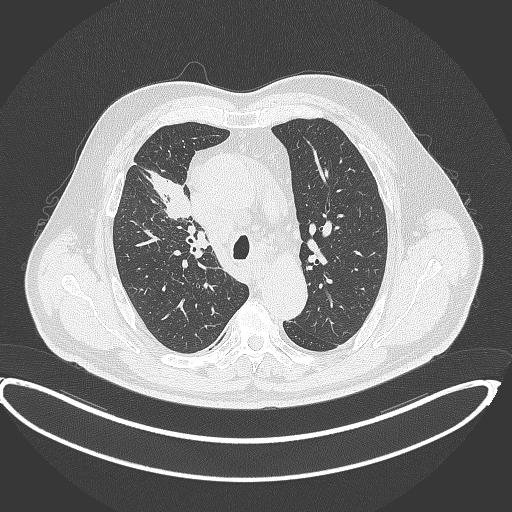
Chest CT, one axial slice. Position 285 of 390 along the scan axis. Lung window (W 1500 / L -600 HU). 1 mm slice thickness. 512 × 512 image matrix, field of view 448 × 448 mm. Patient: male, 62 years. Case-level facts recorded for this patient, not image findings: clinical TNM (as recorded): T1c N3 M1c.
Structures marked on this image (rectangle marked by the reading radiologist):
- lung tumour (recorded histology: adenocarcinoma): bounding box <148,166,194,221> (left, top, right, bottom; pixels)